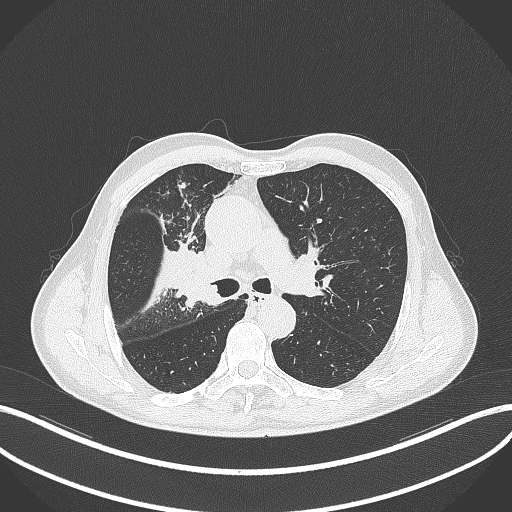
Chest CT, one axial slice. Slice 311 of 490 in the series (ordered by position). Reconstruction kernel B70f. 120 kVp. Lung window (W 1500 / L -600 HU). 1 mm slice thickness. 512 × 512 image matrix, field of view 400 × 400 mm. Patient: male, 69 years. From the clinical record (not read from this slice): clinical TNM (as recorded): T2a N0 M0.
Annotated regions visible in this slice (bounding box drawn by a radiologist):
- lung tumour (recorded histology: adenocarcinoma): bounding box (x1, y1, x2, y2) in pixels: (173, 236, 223, 307)